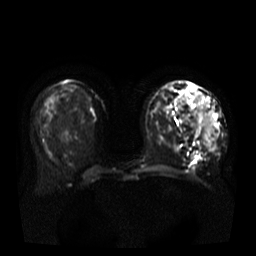
Breast MRI, one axial slice. Position 17 of 37 along the scan axis. Diffusion-weighted series; image 2 of 4 stored at this slice position (different b-values; order by instance number). 3 T. 256 × 256 image matrix, field of view 380 × 380 mm. Female patient.
Structures marked on this image (manually delineated by an expert):
- tumour on diffusion-weighted imaging: bounding box (x1, y1, x2, y2) in pixels: (195, 91, 217, 151)